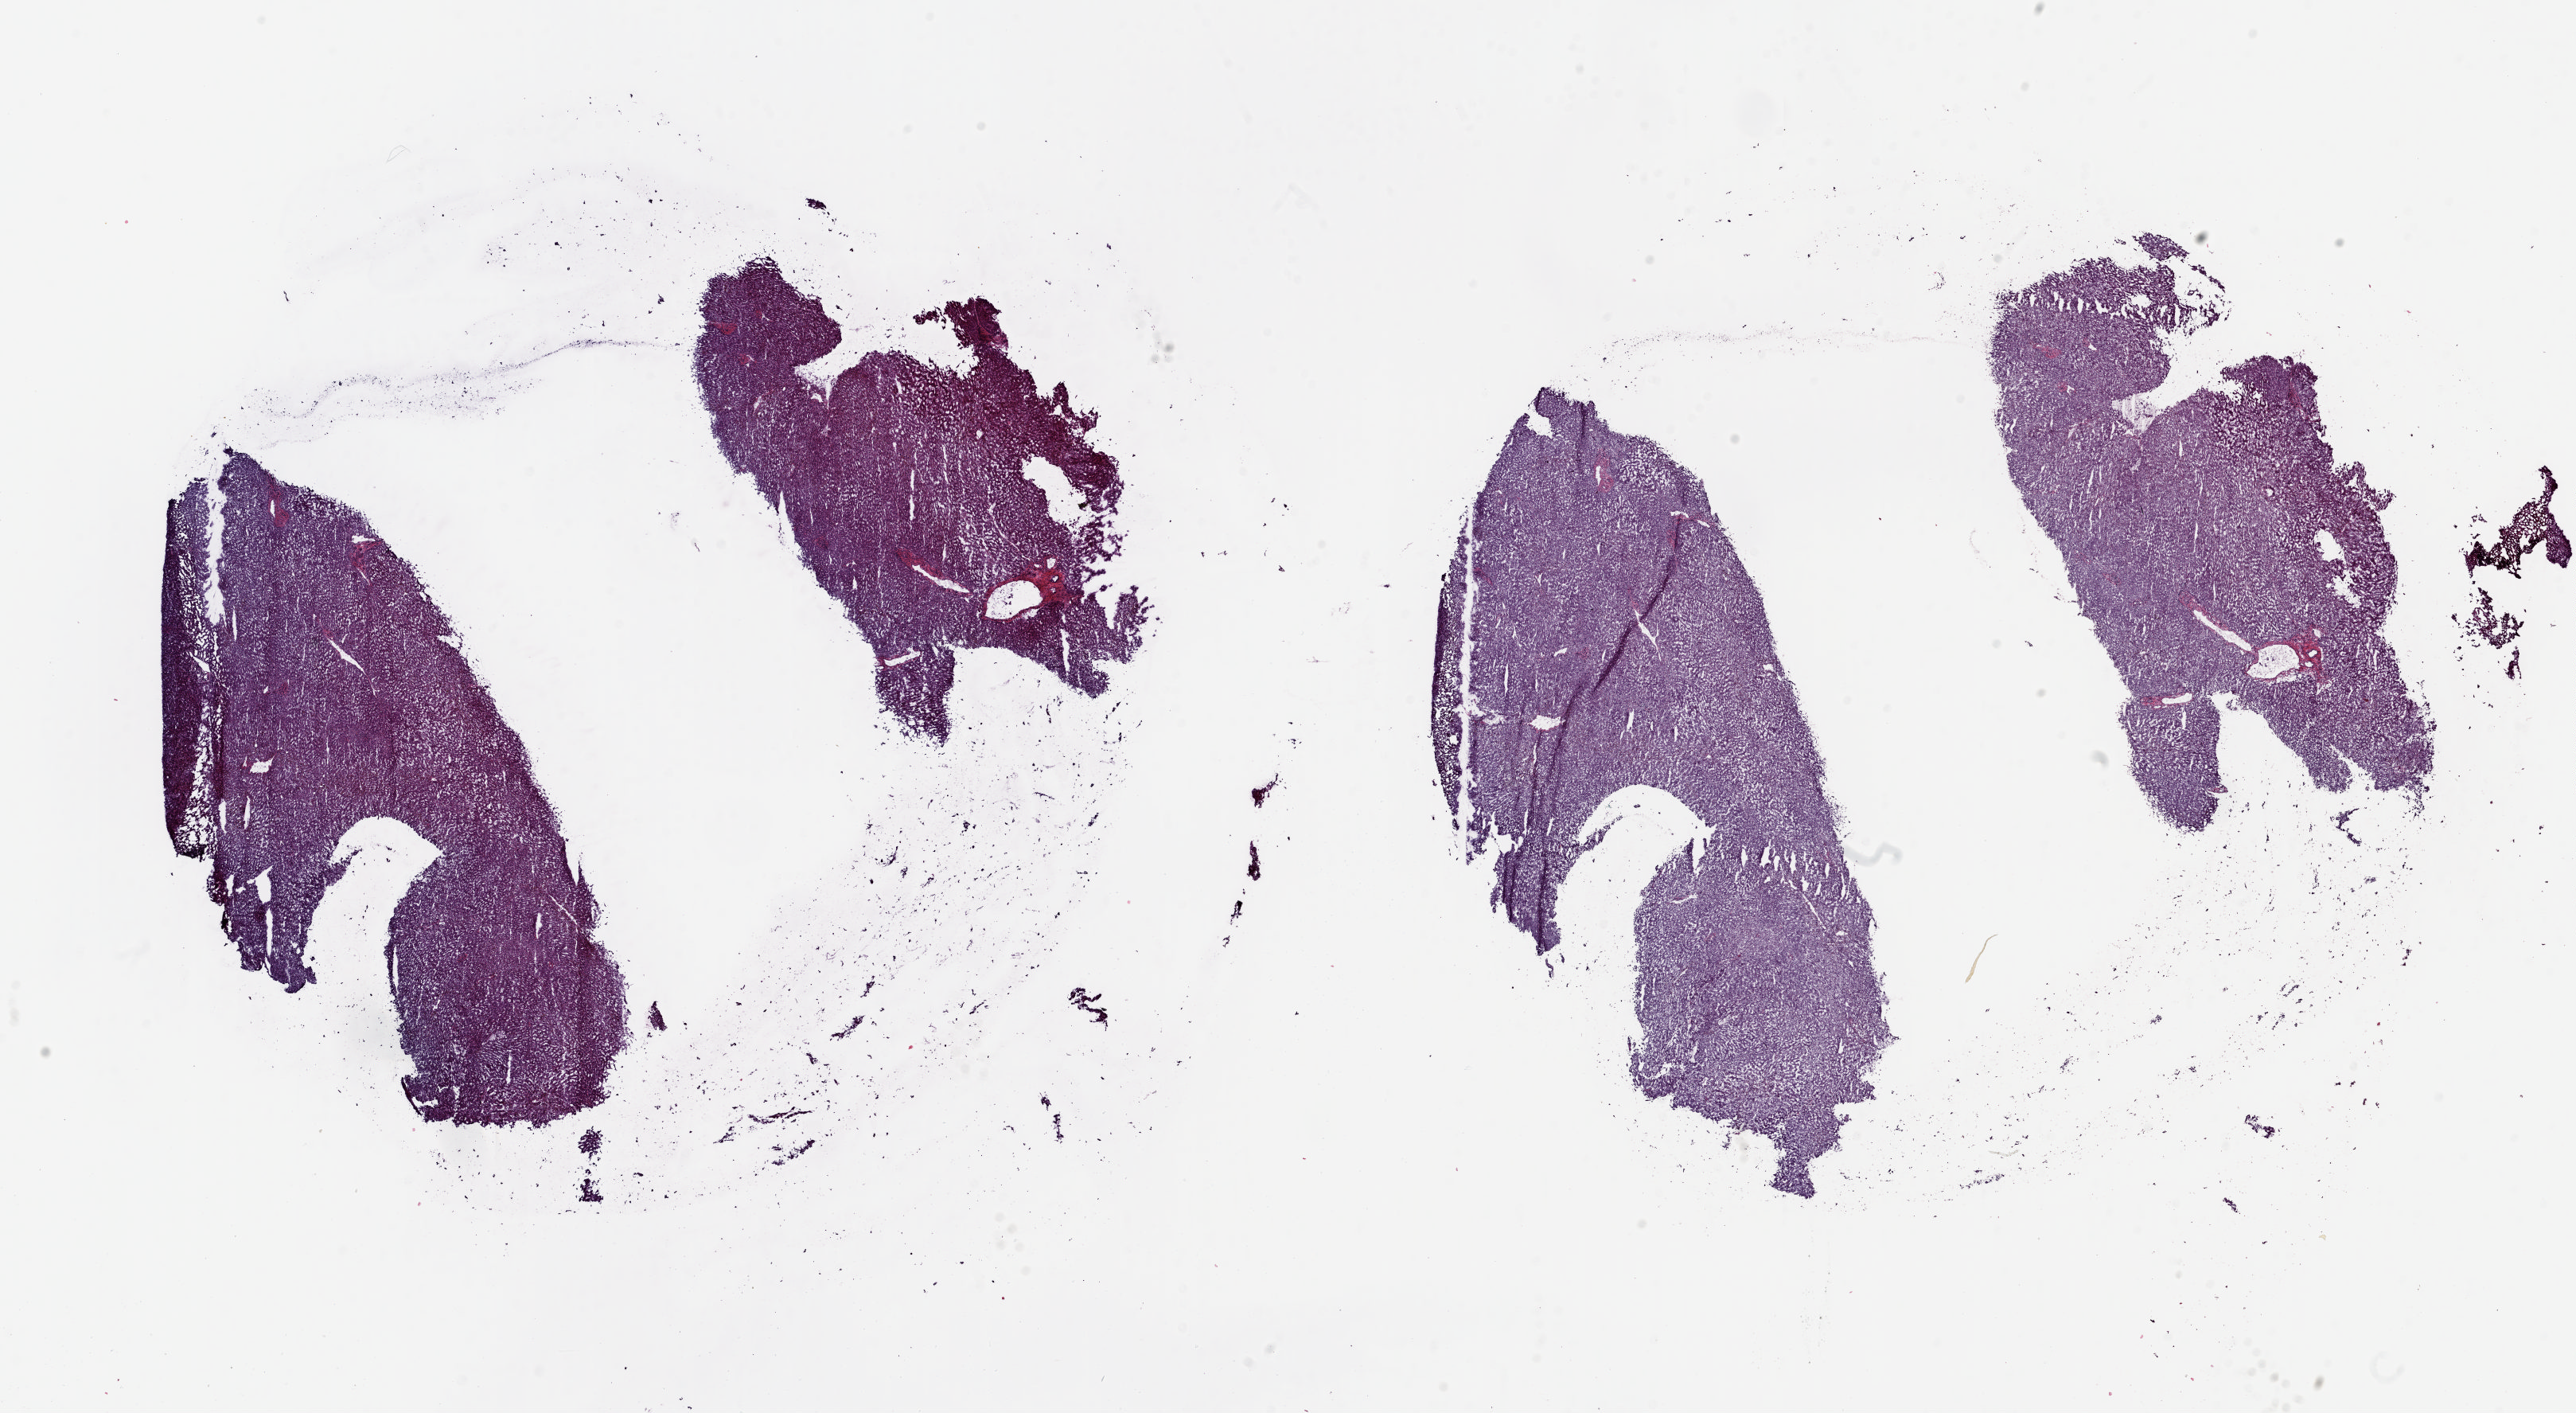
Digitized H&E tissue section (whole slide) — shown as a low-resolution overview of the whole scanned area (about 25.7 x 14.1 mm, slide scanned at 20x); frozen section from the top of the tissue portion; liver, solid tissue normal (non-tumour tissue) sample. Female patient; age at initial diagnosis 66 years. Slide review estimates, as recorded: tumour cells 0%, tumour nuclei 0%, normal cells 100%, stromal cells 0%, necrosis 0%. Inflammatory infiltration, as recorded: lymphocyte infiltration 0%, monocyte infiltration 0%, neutrophil infiltration 0%.
This section: solid tissue normal (non-tumour) sample from the same patient. Patient diagnosis: Hepatocellular carcinoma, NOS.